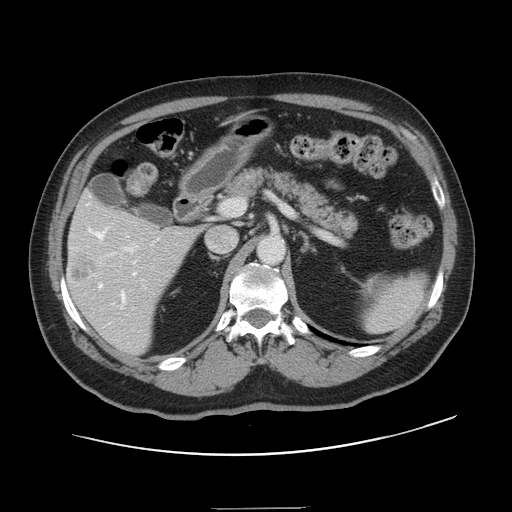
Contrast-enhanced abdominal CT, one axial slice. Position 79 of 143 along the scan axis. 120 kVp. Intravenous contrast given. Soft-tissue window (W 400 / L 40 HU). 512 × 512 image matrix. Male patient, age 62 years. Case-level facts recorded for this patient, not image findings: diagnosis: colorectal cancer liver metastases, imaged before liver resection; multiple liver metastases: yes; largest metastasis: 2.7 cm.
Annotated regions visible in this slice (expert manual segmentation):
- hepatic veins: bounding box <88,203,136,301> (left, top, right, bottom; pixels)
- liver: <67,195,197,354>
- planned liver remnant (the part of the liver to remain after resection): <72,195,137,231>
- portal vein (with intrahepatic branches): <108,247,136,305>
- liver metastasis: <73,262,94,281>